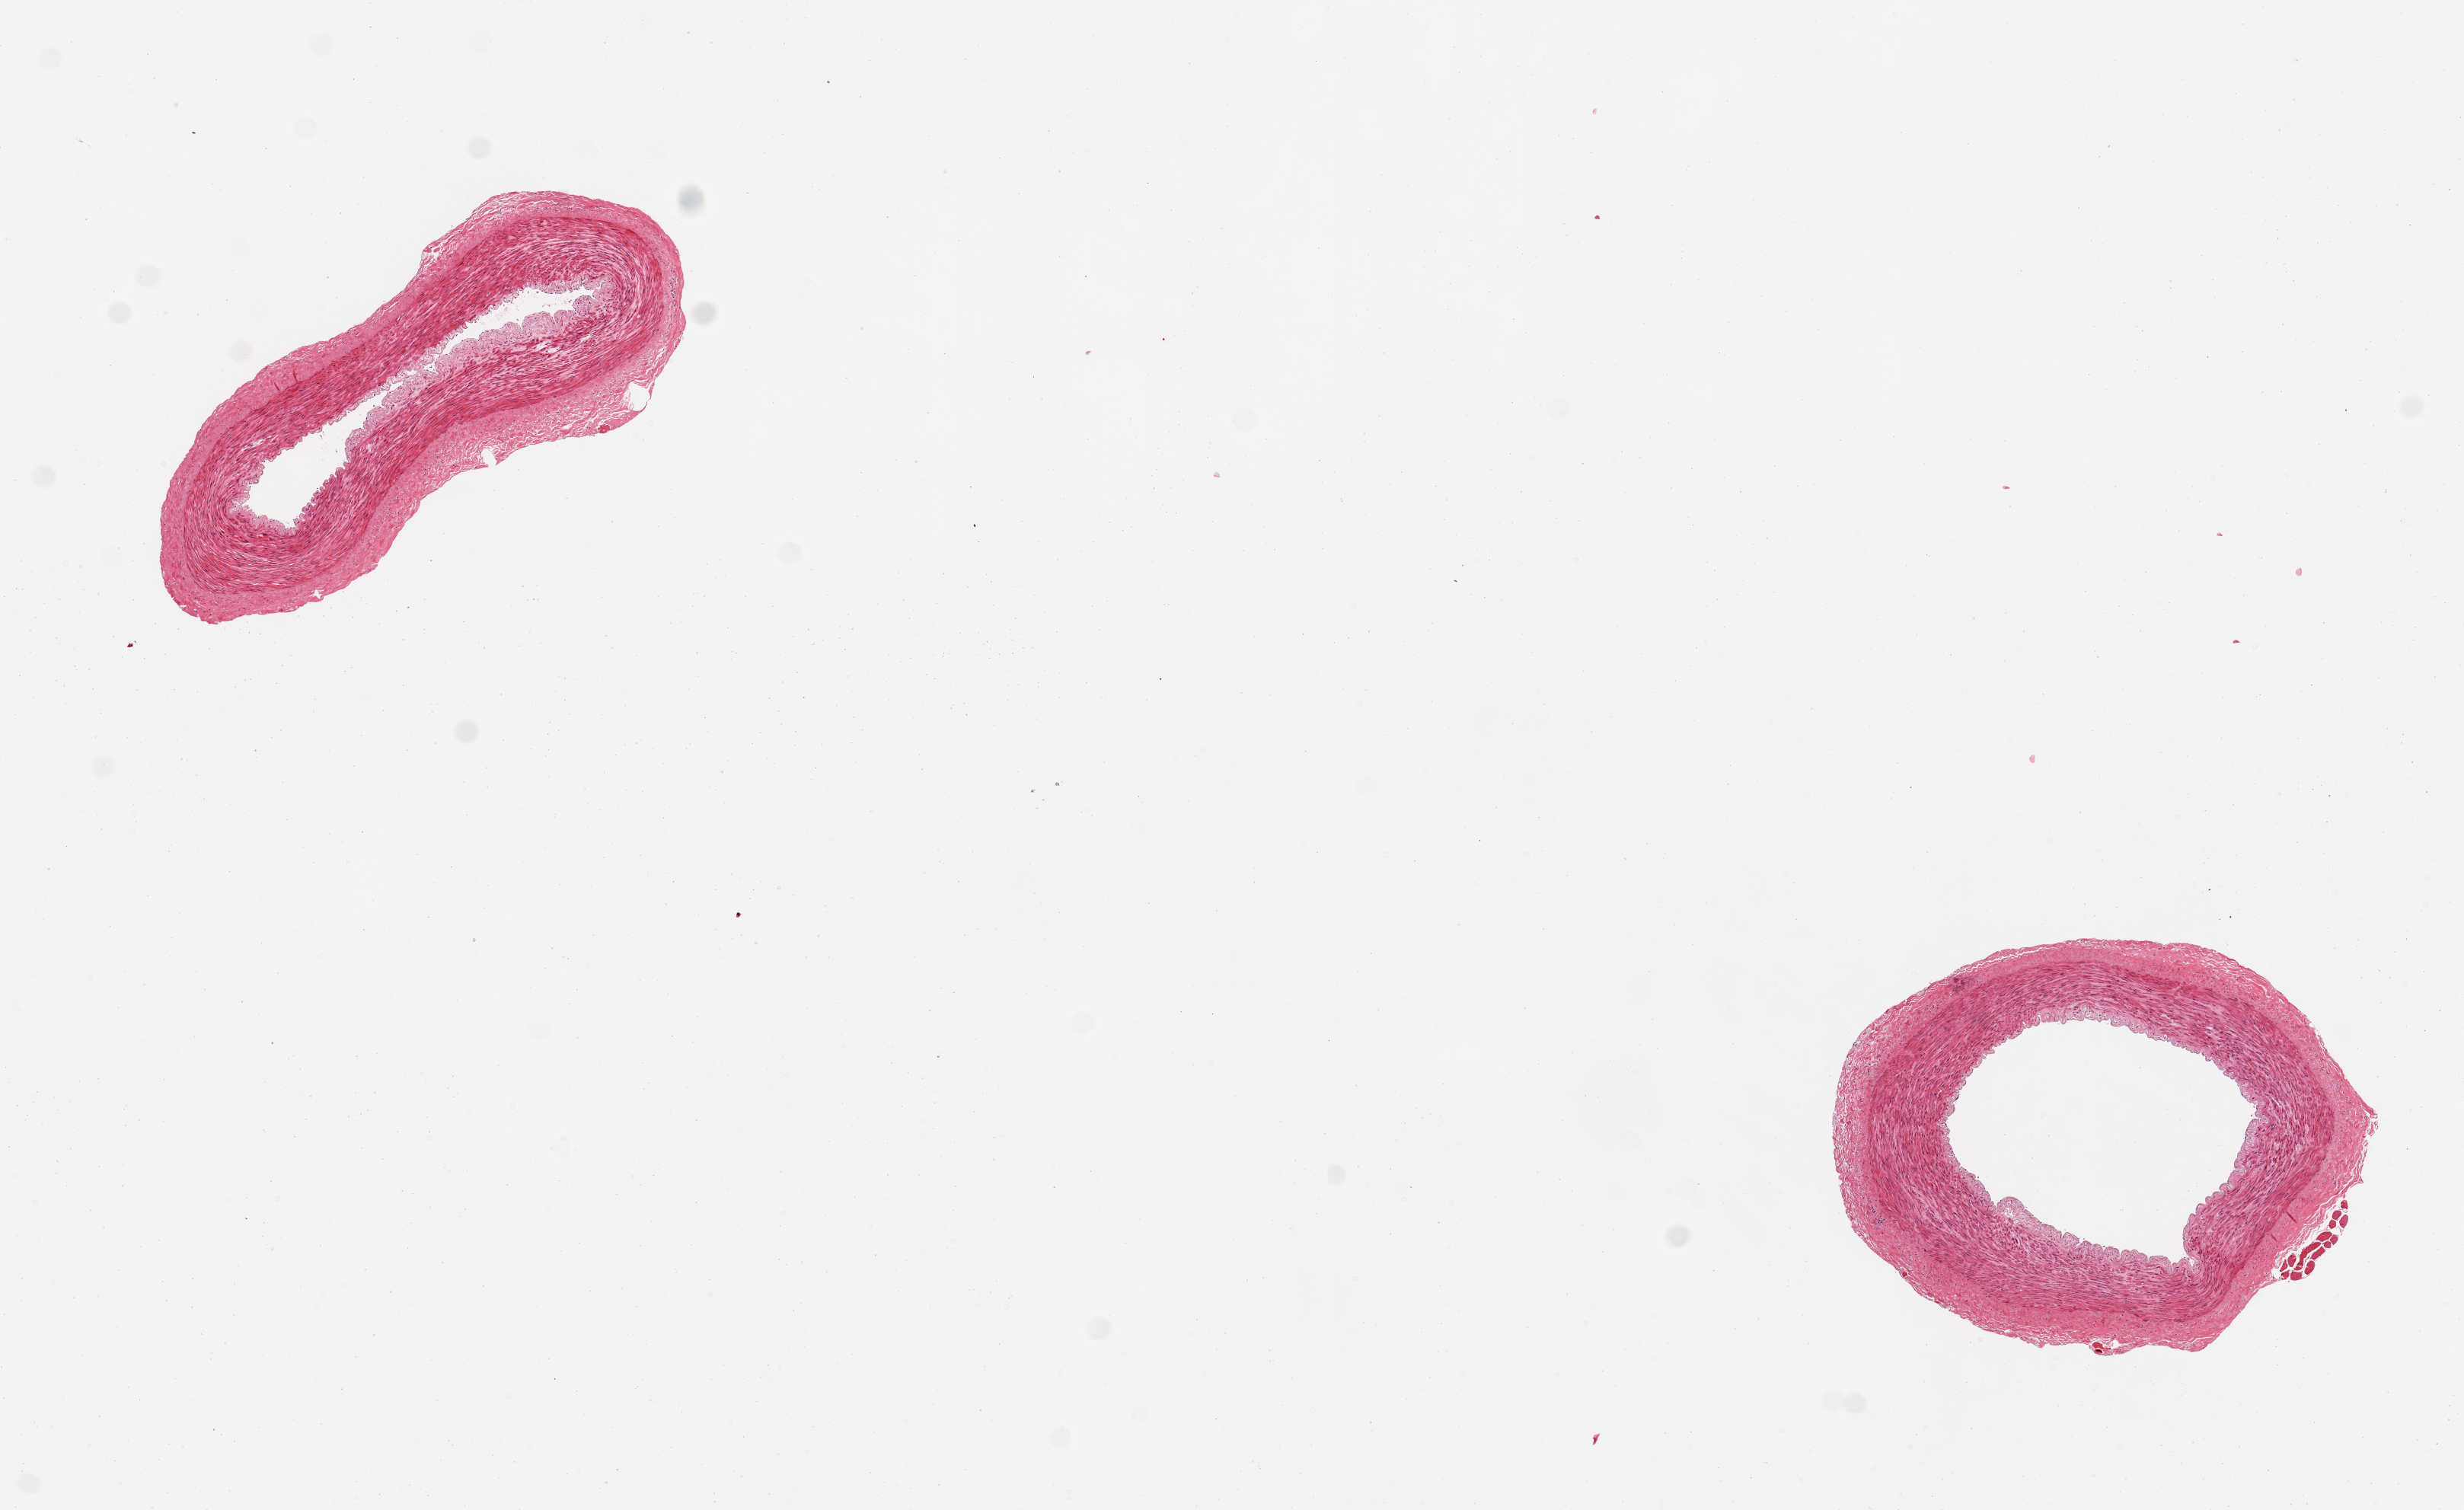
Haematoxylin and eosin whole-slide image, shown as a low-resolution overview of the whole scanned area (about 12.8 x 7.8 mm). PAXgene-fixed paraffin-embedded (PFPE) section. Section of tibial artery (target tissue). Tissue donor sample. Female donor.
Pathologist's review note for this sample: 2 pieces; well trimmed, small fragment of skeletal muscle.